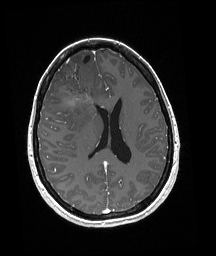
Brain MRI from a brain-tumour surgery series, one axial slice; slice 82 of 192 in the series (ordered by position); T1-weighted post-contrast; 1 mm slice thickness; 216 × 256 image matrix, field of view 211 × 250 mm. Case-level facts recorded for this patient, not image findings: histopathology: Oligodendroglioma; WHO grade: 3; IDH mutation: yes; tumour location: Right Frontal.
Outlined on this slice (expert manual segmentation):
- tumour: bounding box [x1, y1, x2, y2] px = [55, 81, 97, 104]